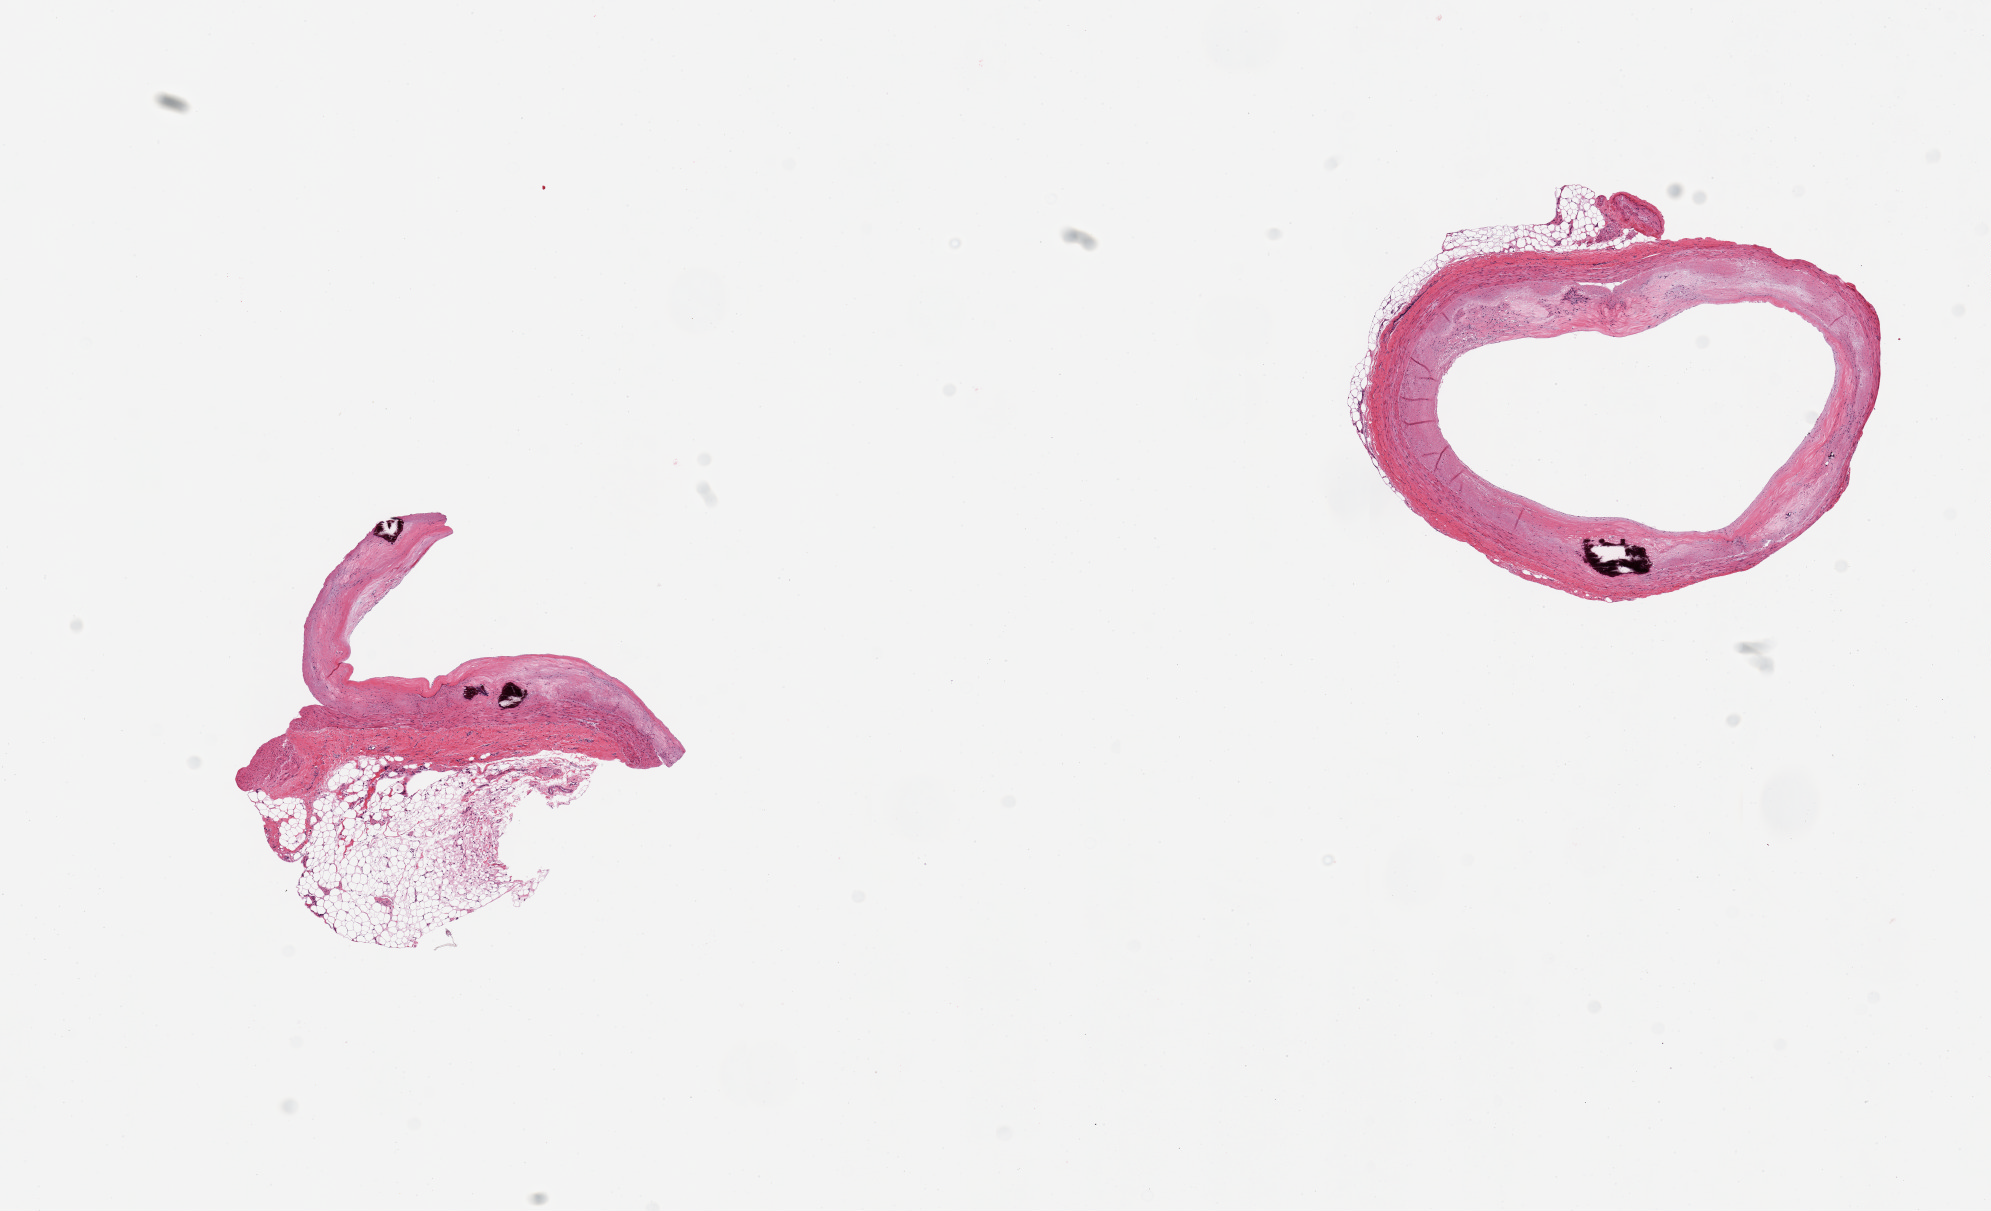
Haematoxylin and eosin whole-slide image, brightfield — shown as a low-resolution overview of the whole scanned area (about 15.8 x 9.6 mm). PAXgene-fixed, paraffin-embedded tissue. Target tissue: coronary artery. Tissue donor sample. Female donor.
- review note (as recorded): 2 pieces, calcific atherosclerosis